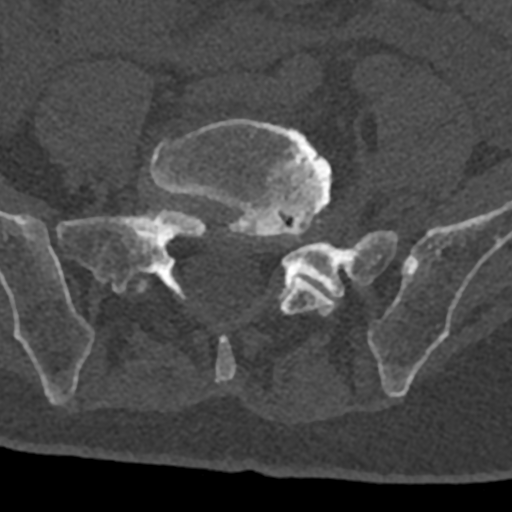
CT including the spine, one axial slice. Slice 176 of 797 in the series (ordered by position). 120 kVp. Bone window (W 1800 / L 400 HU). 0.5 mm slice thickness. 512 × 512 image matrix, field of view 160 × 160 mm. Male patient, age 74 years. Case-level facts recorded for this patient, not image findings: primary cancer: renal; vertebrae with lytic lesions (as recorded): T10, L1, L2, L3, L4, L5.
Structures marked on this image (semi-automatic segmentation, software-assisted and operator-edited):
- L5 vertebra: box from (x=137, y=118) to (x=351, y=383) px